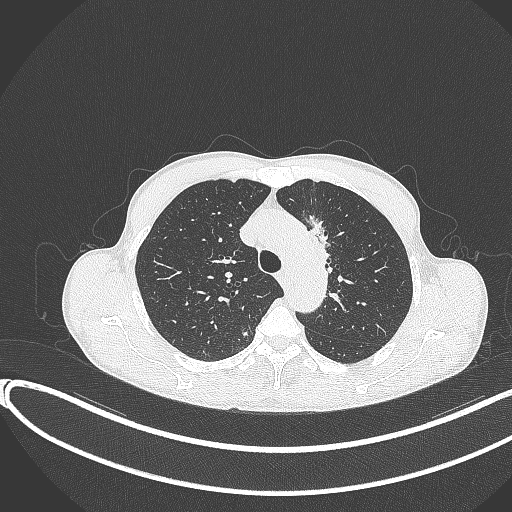
Chest CT, one axial slice. 120 kVp. Lung window (W 1500 / L -600 HU). 1 mm slice thickness. 512 × 512 image matrix, field of view 400 × 400 mm. Patient: male, 58 years. Case-level facts recorded for this patient, not image findings: clinical TNM (as recorded): T1c N1 M0.
Outlined on this slice (bounding box drawn by a radiologist):
- lung tumour (recorded histology: adenocarcinoma): bounding box [x1, y1, x2, y2] px = [300, 211, 337, 274]